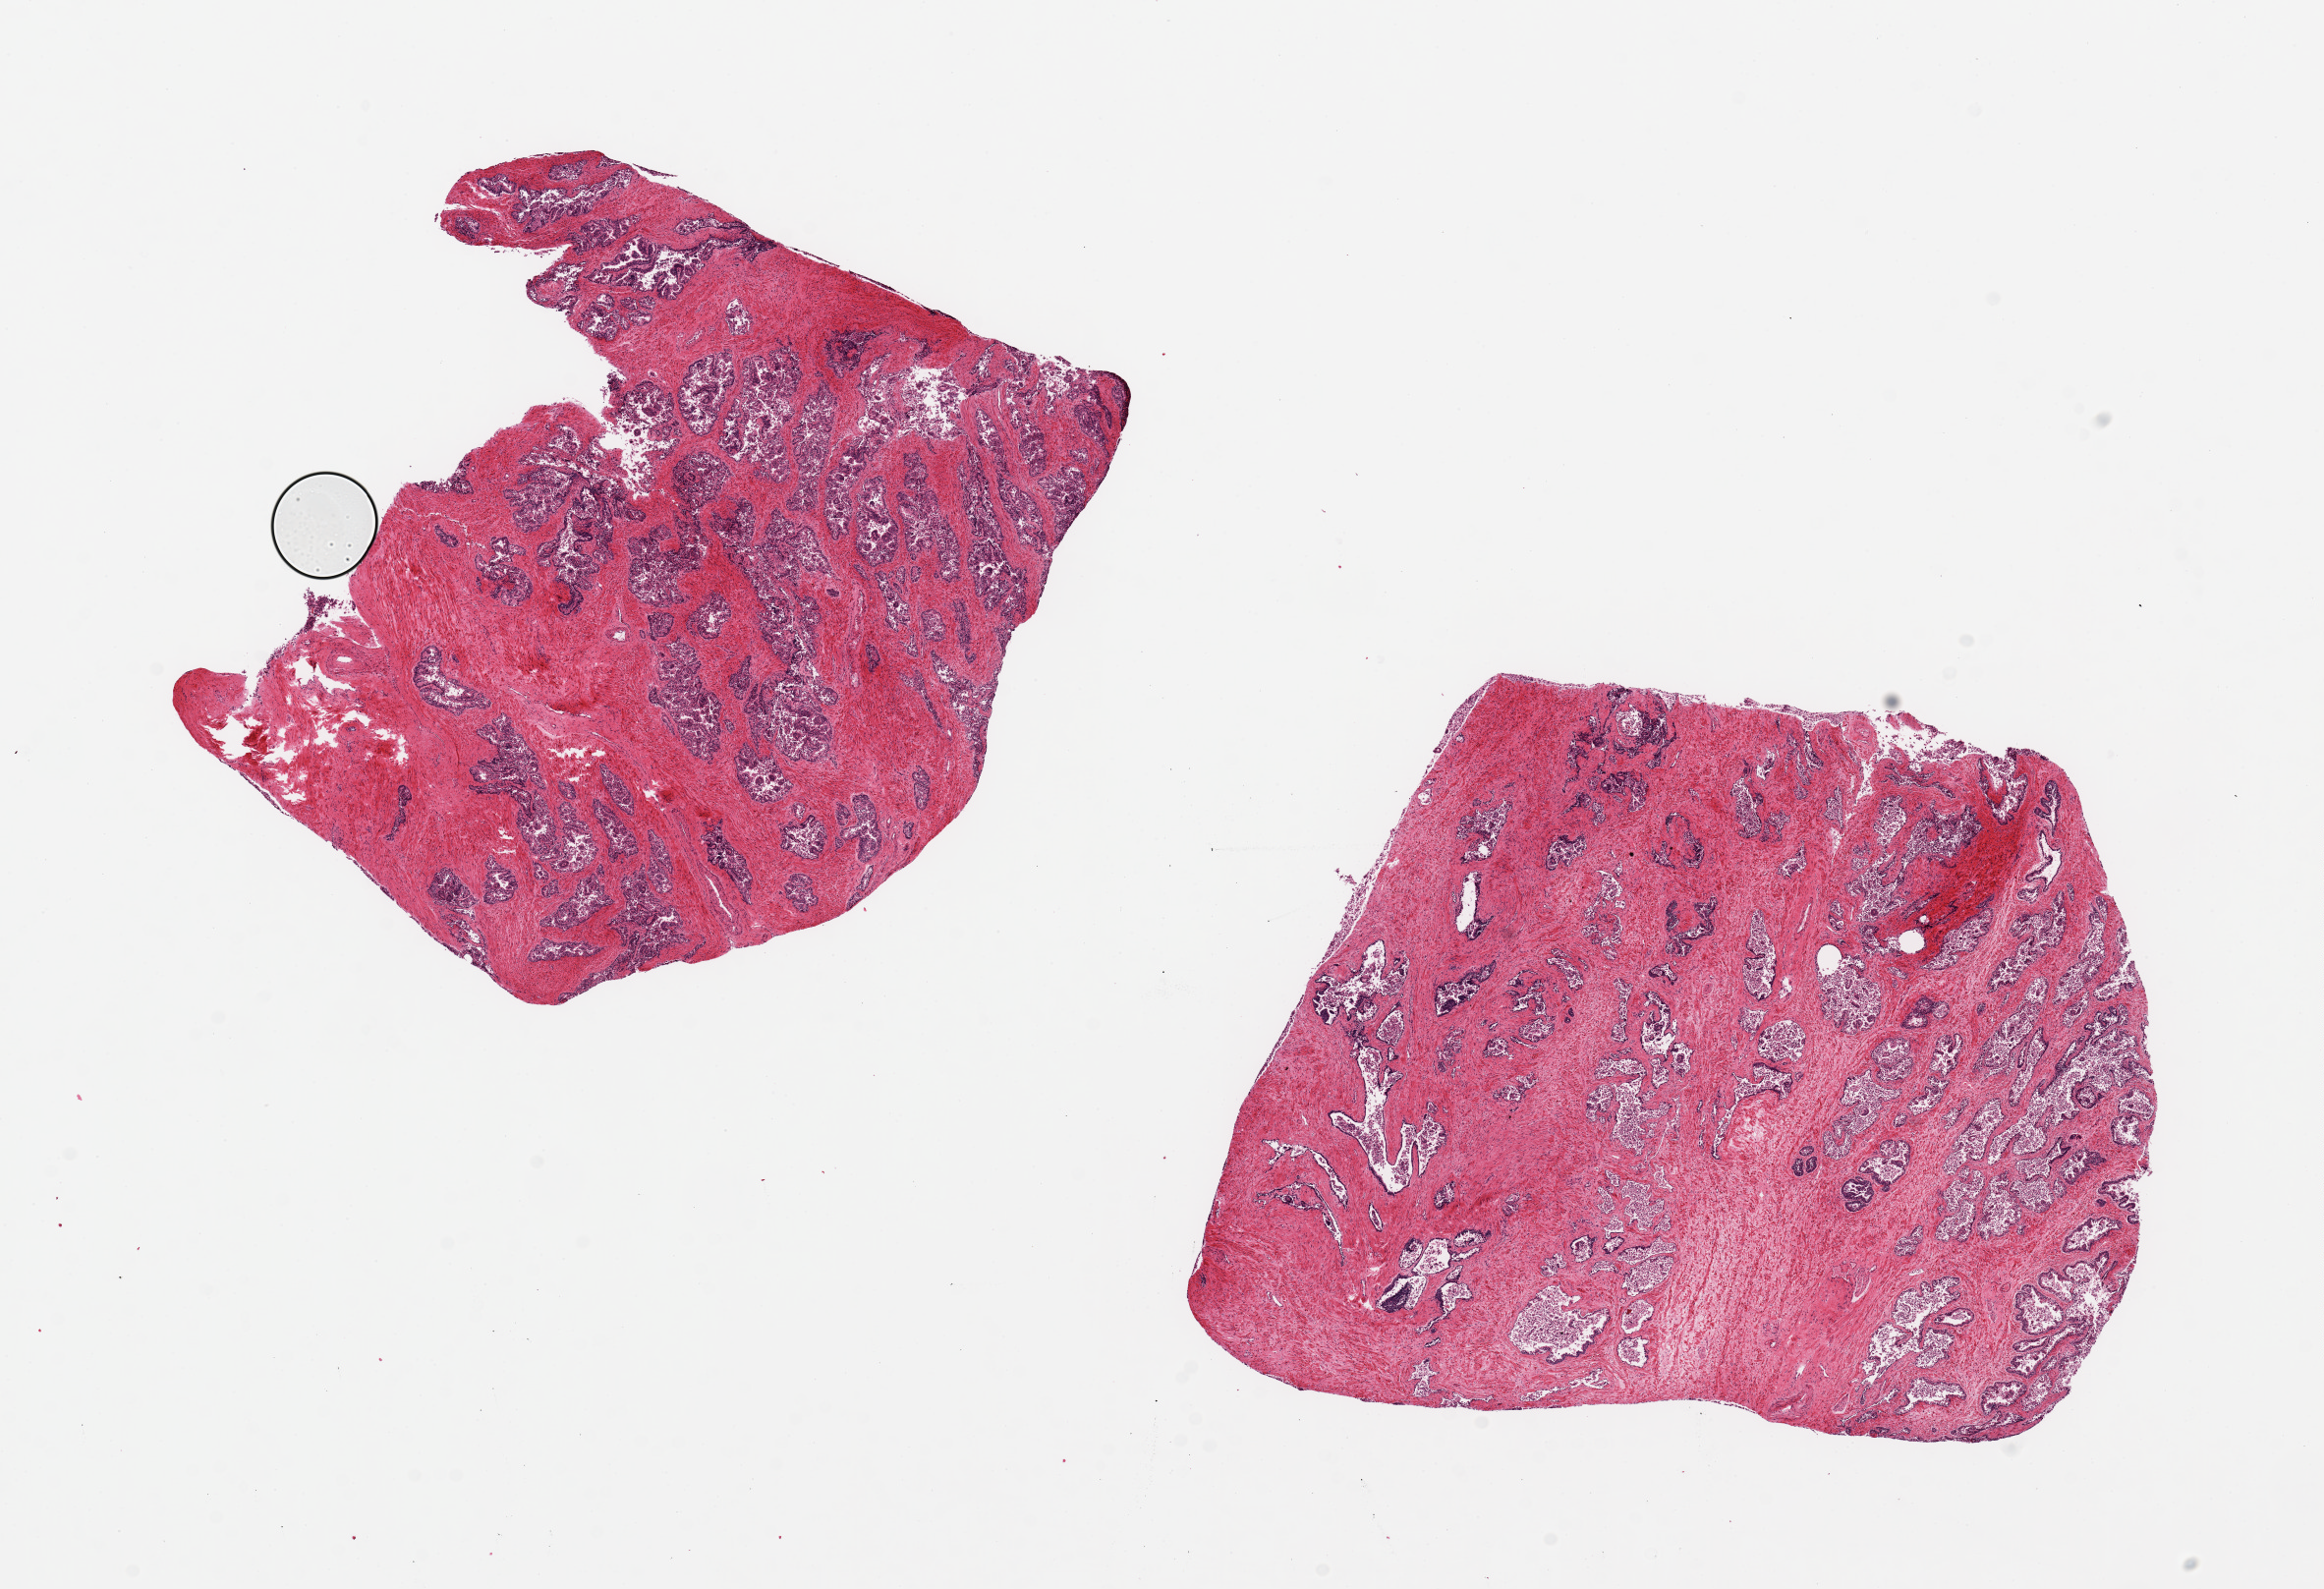
Hematoxylin and eosin (H&E) whole-slide image — shown as a low-resolution overview of the whole scanned area (about 18.7 x 12.8 mm, acquisition: 20x scan). PAXgene-fixed, paraffin-embedded tissue. Sampled site (target tissue): prostate. Donor tissue sample. Donor sex: male.
Reviewer comment on this tissue sample: 2 pieces ~7x6mm. Glandular hyperplasia, mucosa poorly preserved.